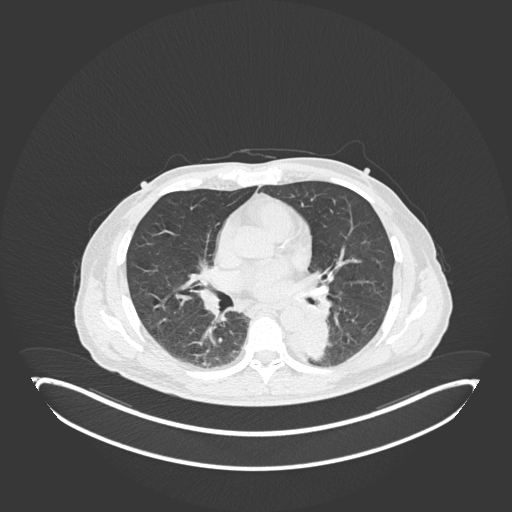
Chest CT, one axial slice; position 101 of 251 along the scan axis; reconstruction kernel B30f; lung window (W 1500 / L -600 HU); 512 × 512 image matrix, field of view 500 × 500 mm. Patient: male, 72 years. Case-level facts recorded for this patient, not image findings: clinical TNM (as recorded): T2b N0 M1.
Structures marked on this image (rectangle marked by the reading radiologist):
- lung tumour (recorded histology: adenocarcinoma): bounding box (x1, y1, x2, y2) in pixels: (290, 318, 329, 364)